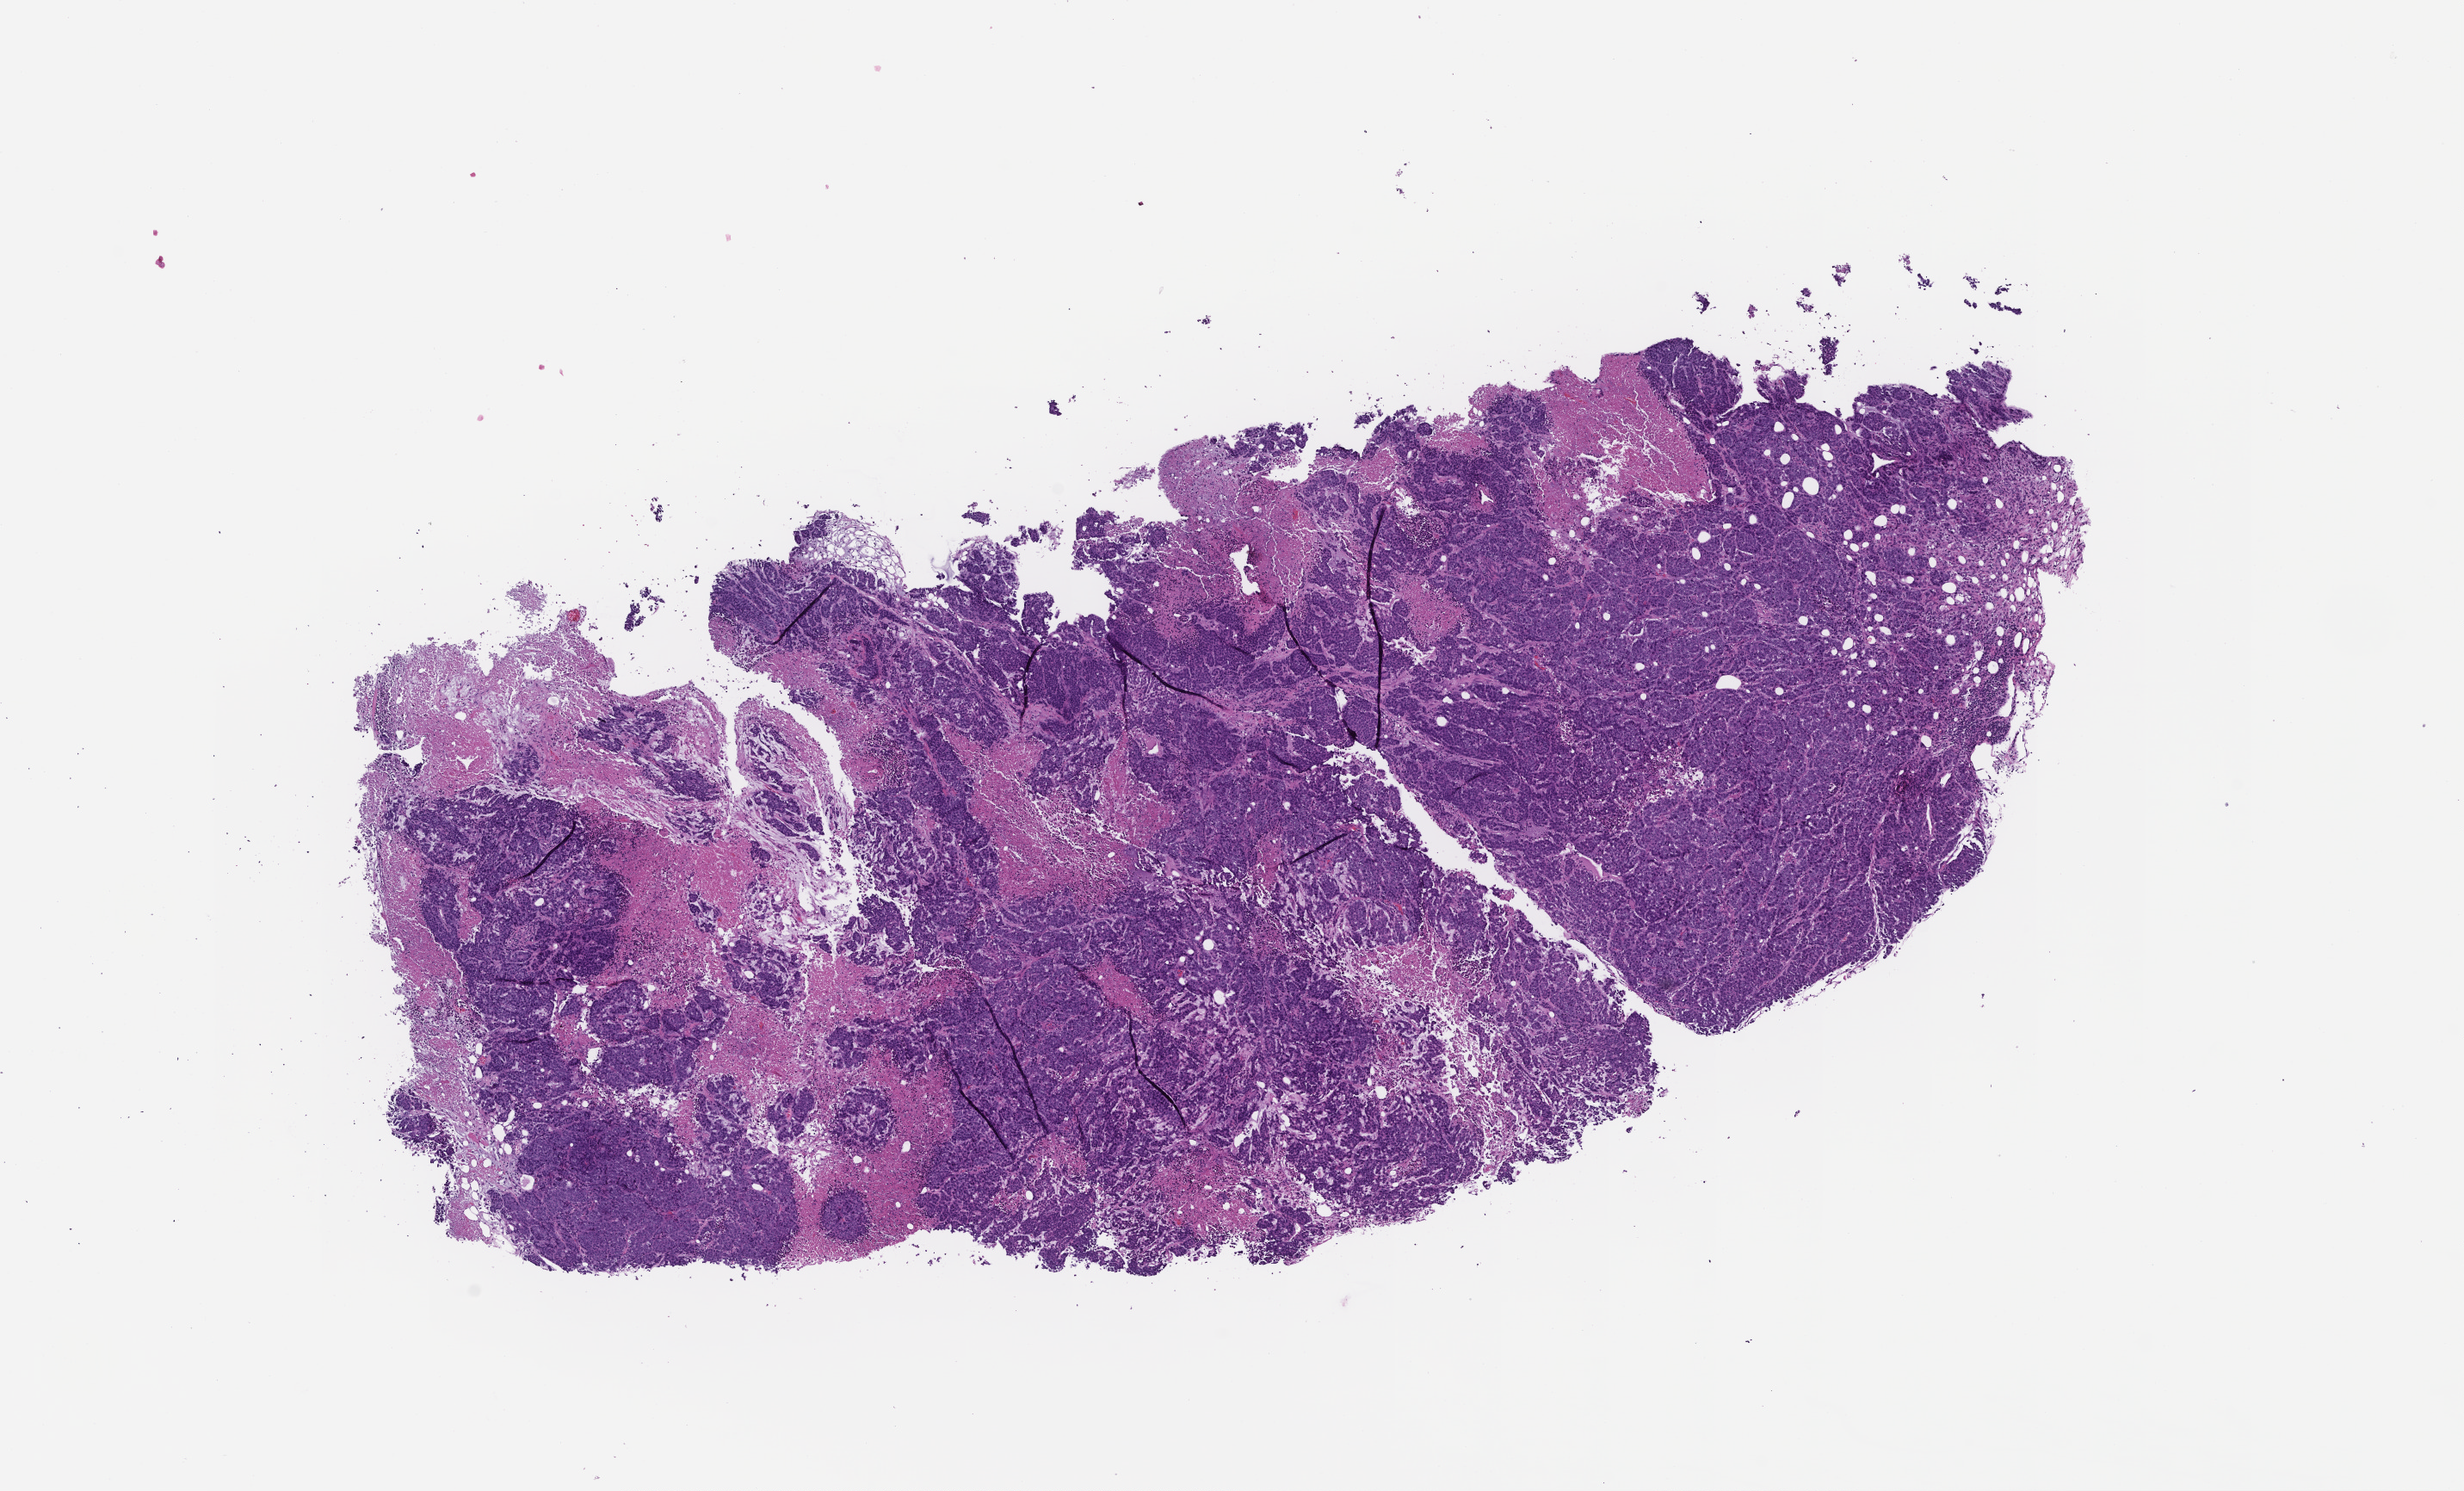
Digitized H&E-stained section, shown as a low-resolution overview of the whole scanned area (about 11.6 x 7.0 mm), formalin-fixed paraffin-embedded section, specimen time point: collected at baseline (before treatment). Patient sex: female.
This section: metastatic tumor tissue. Primary diagnosis of the patient: Colorectal Carcinoma.